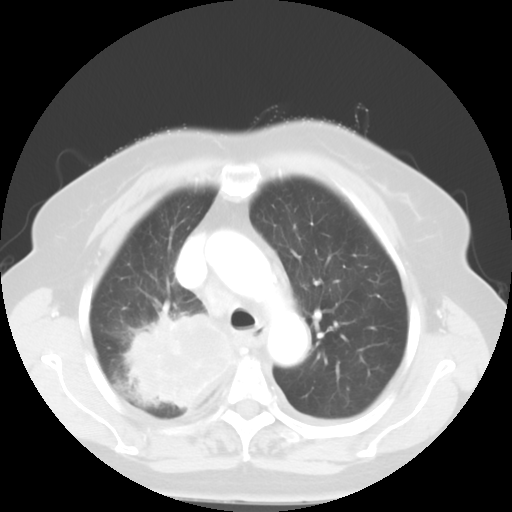
Chest CT, one axial slice. Slice 39 of 52 in the series (ordered by position). Reconstruction kernel STANDARD. 120 kVp. Lung window (W 1500 / L -600 HU). 5 mm slice thickness. 512 × 512 image matrix, field of view 333 × 333 mm. Patient: female, 81 years. Case-level facts recorded for this patient, not image findings: clinical TNM (as recorded): T4 N3 M1b.
Annotated regions visible in this slice (bounding box drawn by a radiologist):
- lung tumour (recorded histology: adenocarcinoma): bounding box <118,301,237,409> (left, top, right, bottom; pixels)